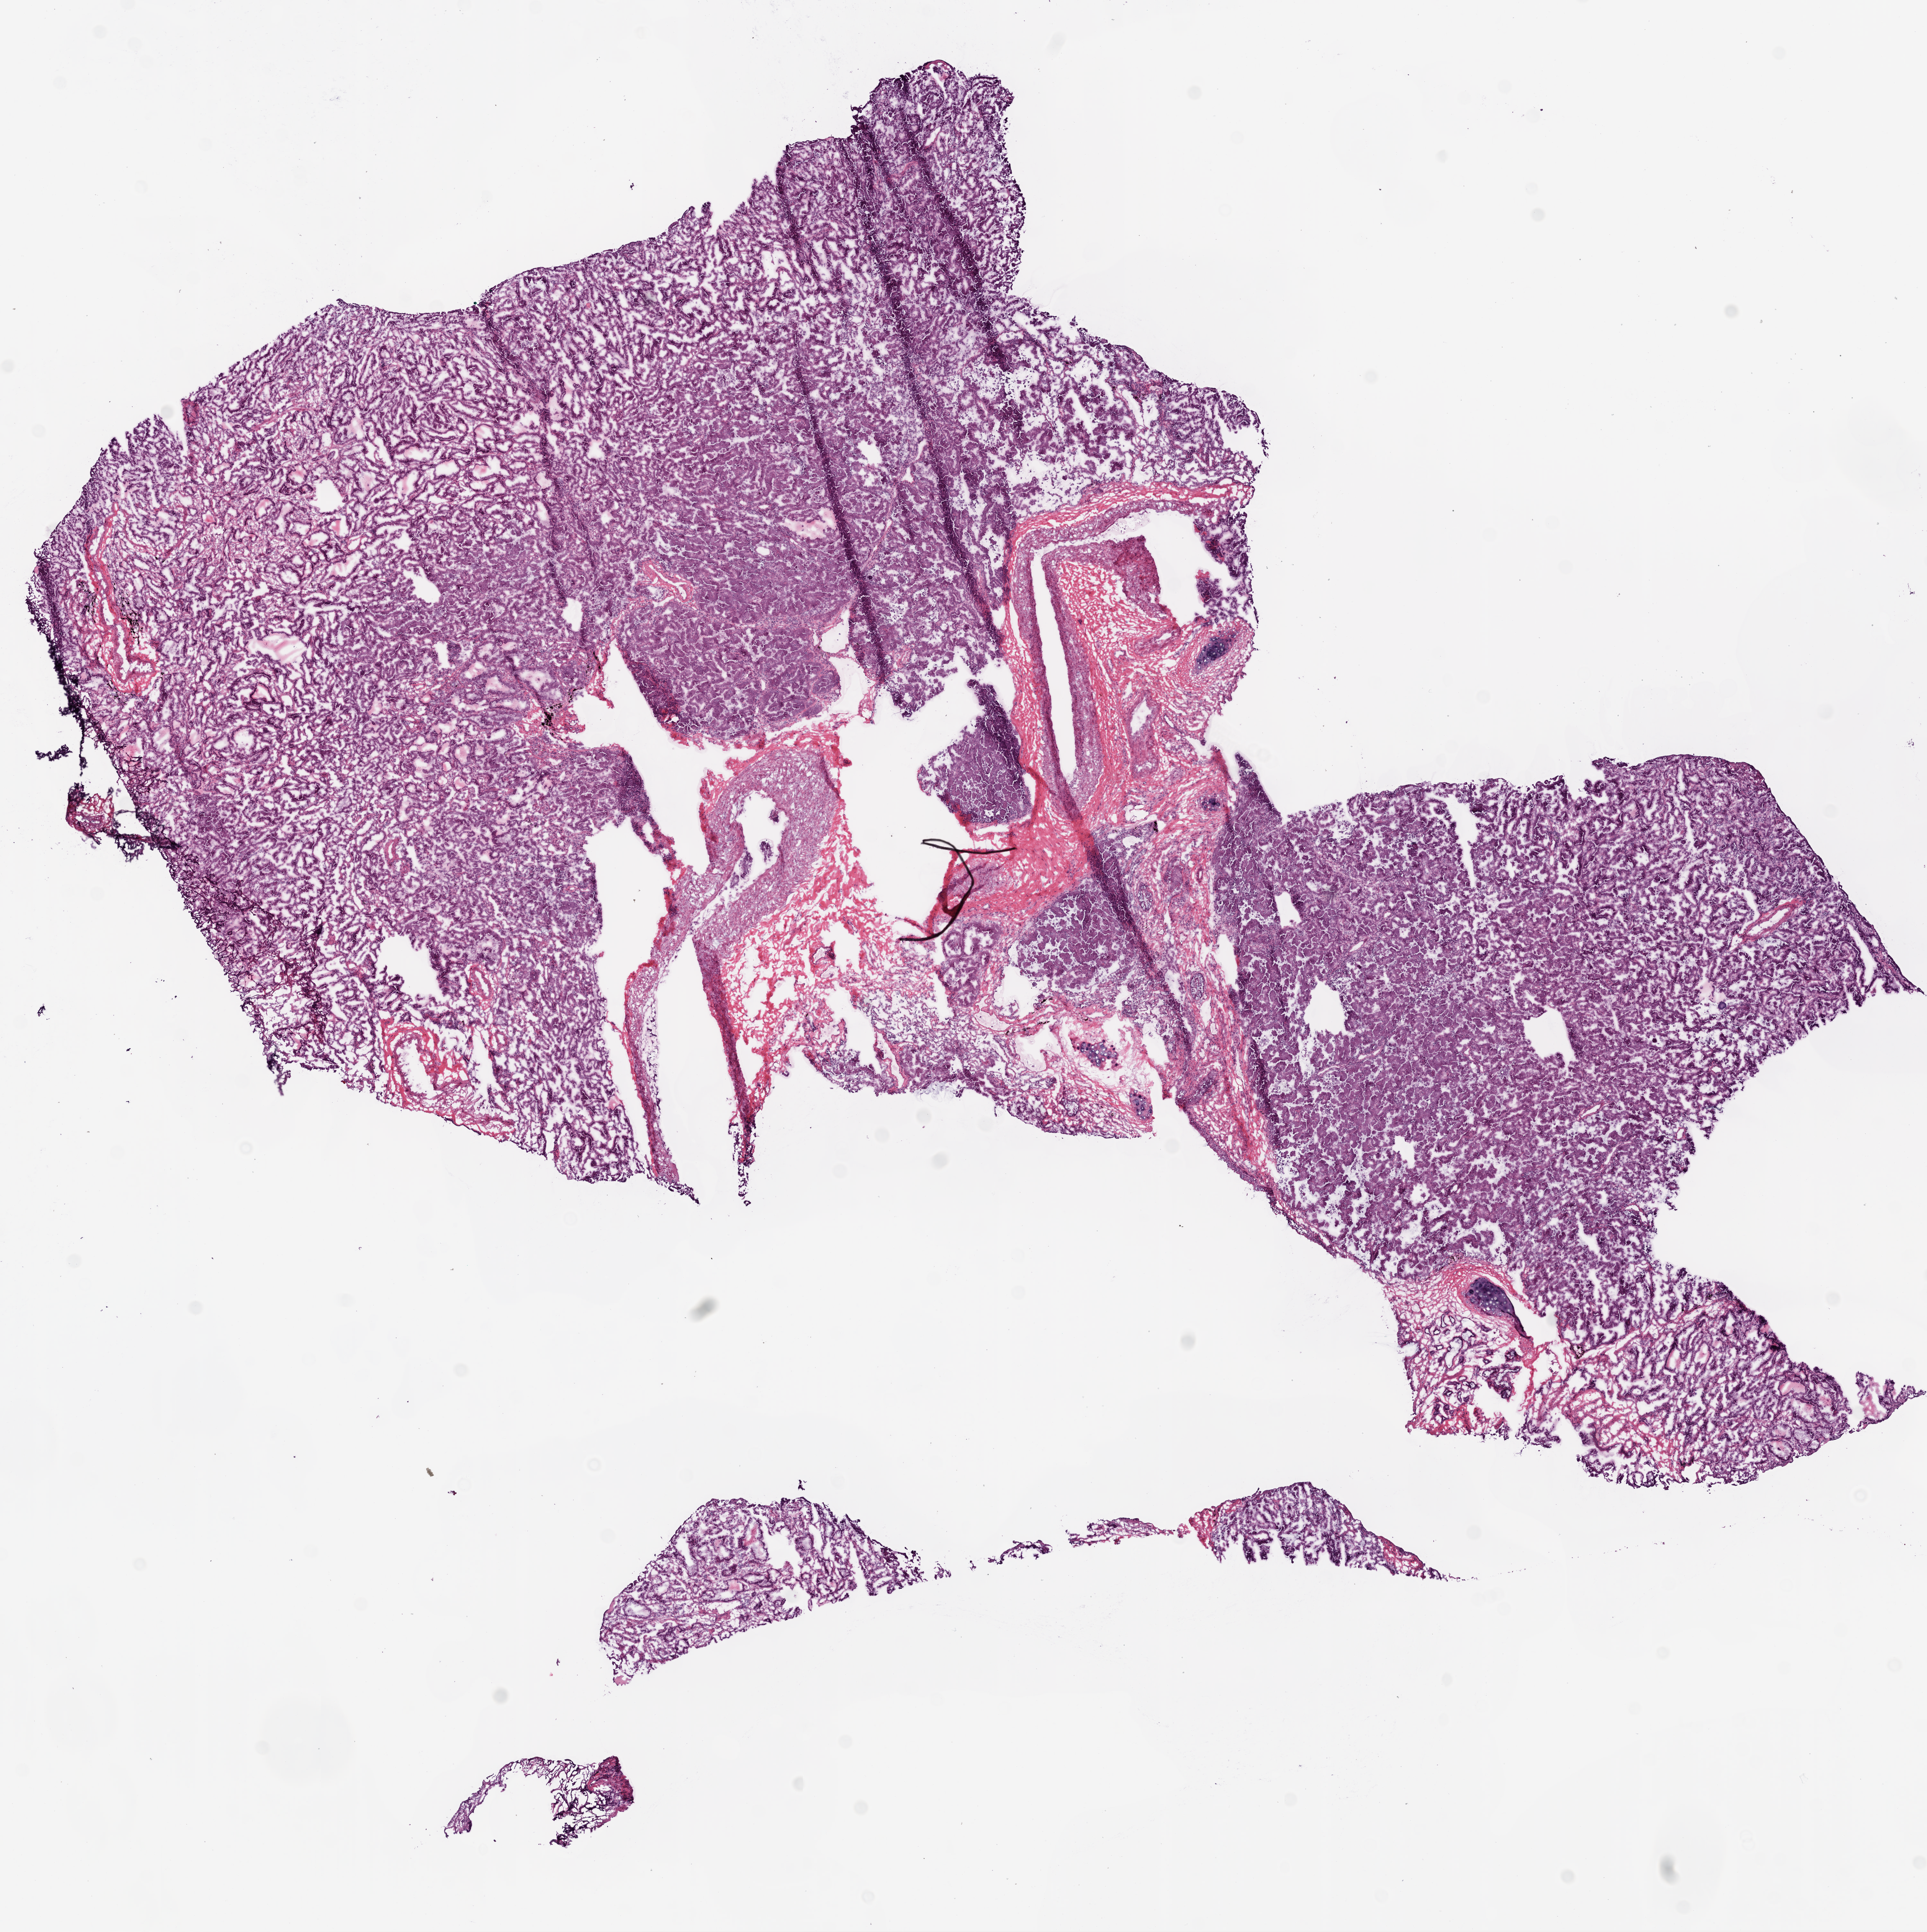
Hematoxylin and eosin (H&E) stained whole-slide image — shown as a low-resolution overview of the whole scanned area (about 12.0 x 12.1 mm, from a 20x scan). Frozen section. Sample: primary tumour, lung. Male patient; age at initial diagnosis 63 years. Slide review estimates, as recorded: tumour cells 84%, tumour nuclei 90%, normal cells 0%, stromal cells 15%, necrosis 1%.
- diagnosis: Adenocarcinoma with mixed subtypes (overlapping lesion of lung)
- TNM: T2a N2 M1
- laterality: right
- AJCC pathologic stage: IV